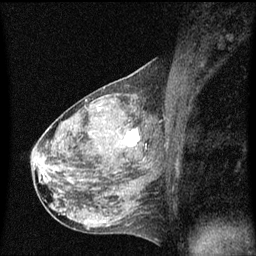
Breast MRI (dynamic contrast-enhanced), one sagittal slice. Position 32 of 60 along the scan axis. Dynamic contrast-enhanced series, image 2 of 3 at this slice position (ordered by acquisition). 1.5 T. TE 4.2 ms, TR 8 ms. 2 mm slice thickness. 256 × 256 image matrix, field of view 200 × 200 mm. Female patient, age 50 years.
Structures marked on this image (semi-automatically segmented with operator editing):
- analysis volume of interest (the breast-tissue region the enhancement analysis was run in; not a lesion): bounding box <106,118,148,159> (left, top, right, bottom; pixels)
- tumour enhancement mask (voxels above the 70 % enhancement threshold inside the analysis volume of interest): <125,128,140,147>